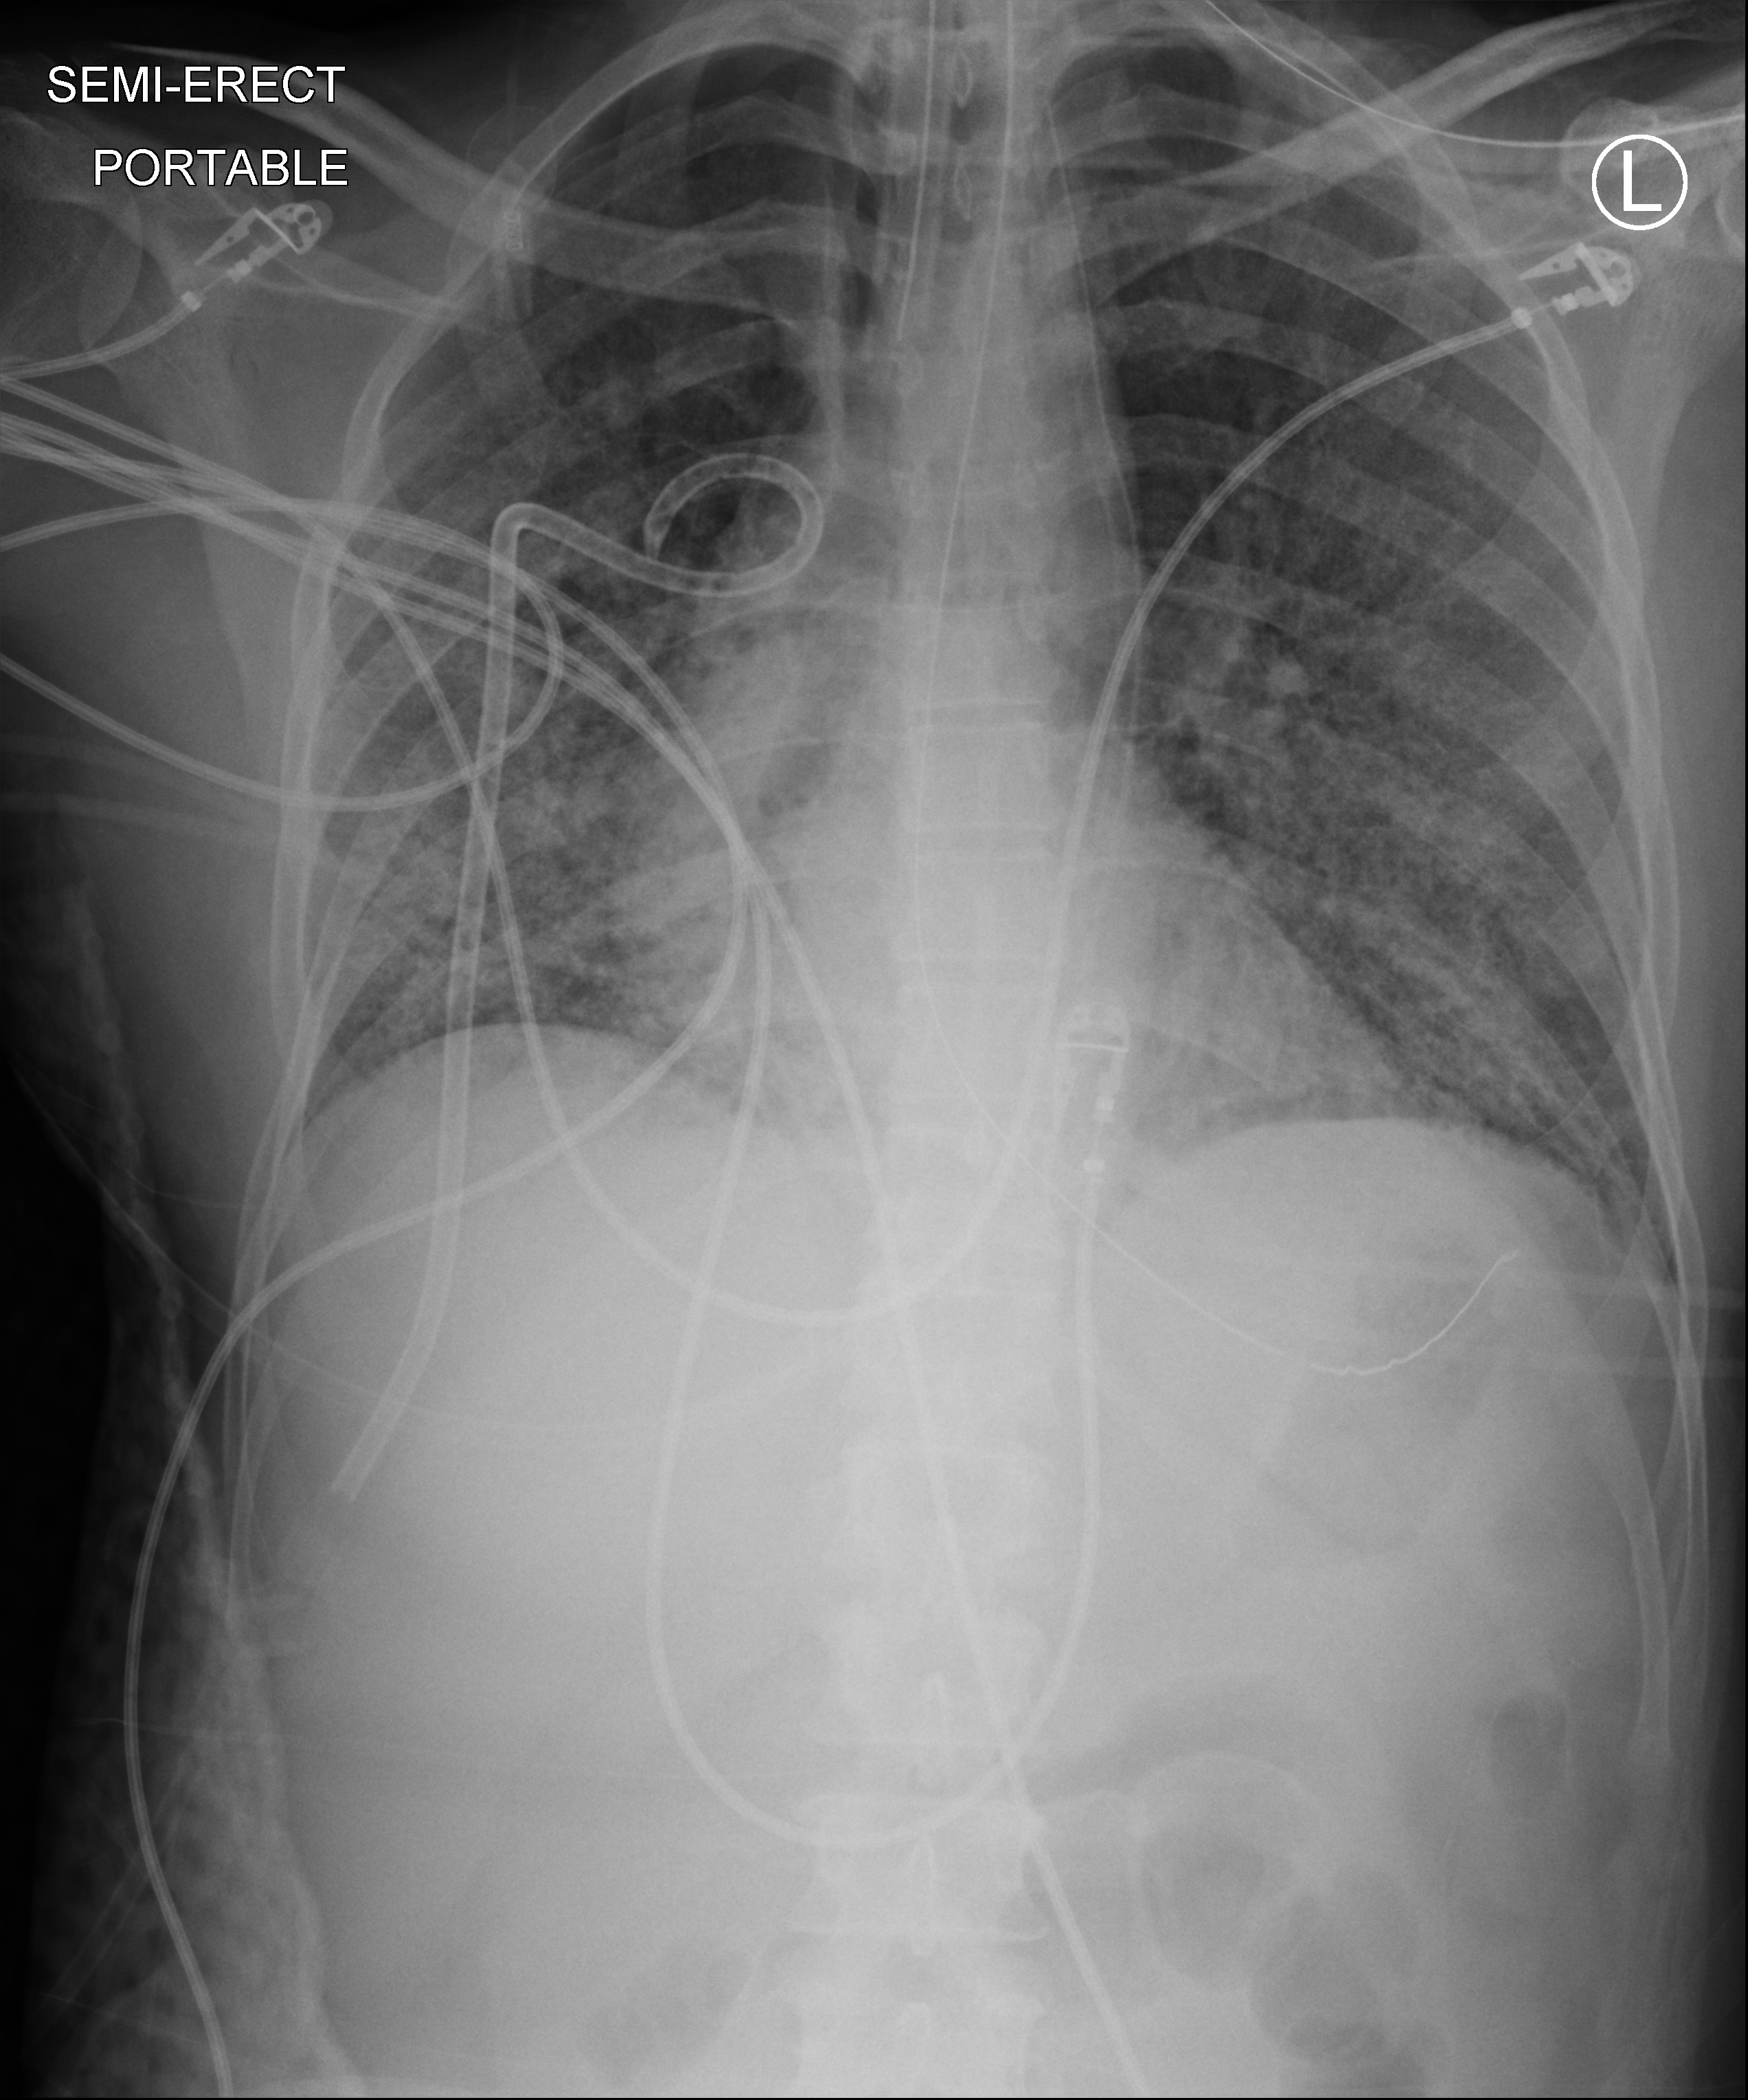
Bedside chest radiograph (computed radiography), anteroposterior (AP) projection. Adult patient hospitalised with COVID-19, age 18–59 years.
Hospital-stay facts (about this admission, not read from this image; timing relative to this image not recorded): diabetes (admission record): no; admitted to intensive care during this hospital stay: yes.